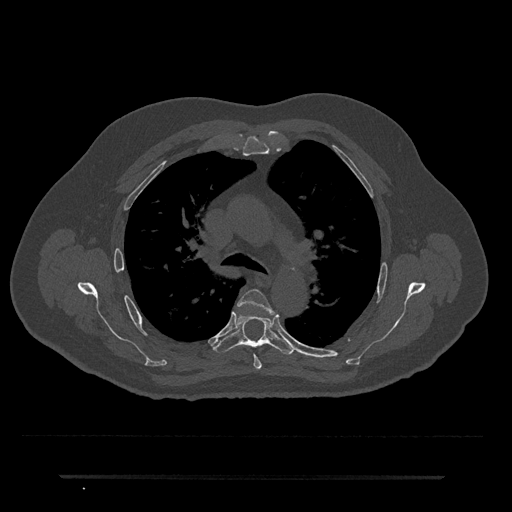
CT including the spine, one axial slice. Slice 499 of 797 in the series (ordered by position). Reconstruction kernel Br40s/3. Bone window (W 1800 / L 400 HU). 0.5 mm slice thickness. 512 × 512 image matrix, field of view 437 × 437 mm. Male patient, age 69 years. Case-level facts recorded for this patient, not image findings: primary cancer: prostate.
Annotated regions visible in this slice (semi-automatic segmentation, software-assisted and operator-edited):
- T4 vertebra: bounding box <238,289,275,369> (left, top, right, bottom; pixels)
- T5 vertebra: <213,314,296,355>